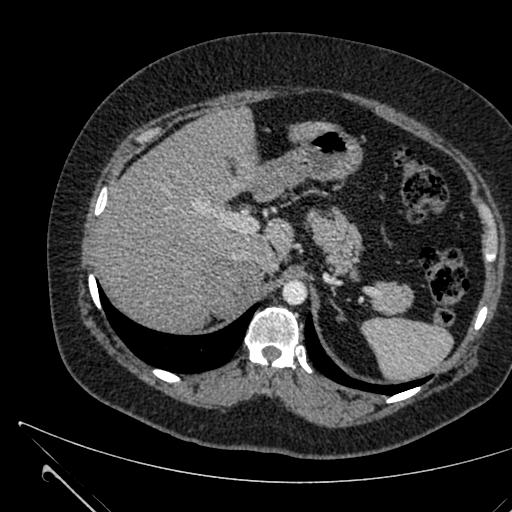
Contrast-enhanced abdominal CT, one axial slice; position 475 of 731 along the scan axis; intravenous contrast given; soft-tissue window (W 400 / L 40 HU); 1 mm slice thickness; 512 × 512 image matrix, field of view 376 × 376 mm. Patient: female, 36 years. Case-level facts recorded for this patient, not image findings: diagnosis: adrenocortical carcinoma; tumour side: right adrenal; tumour size at pathology: 10 cm; Ki-67 index: 20 %; stage (as recorded): 4.
Structures marked on this image (semi-automatically segmented with operator editing):
- mass: bounding box [x1, y1, x2, y2] px = [209, 263, 259, 315]